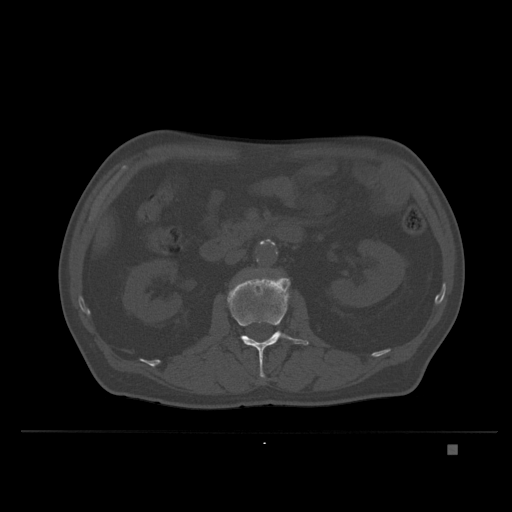
CT including the spine, one axial slice. Position 116 of 435 along the scan axis. Bone window (W 1800 / L 400 HU). 512 × 512 image matrix, field of view 434 × 434 mm. Male patient, age 73 years. From the clinical record (not read from this slice): primary cancer: skin.
Structures marked on this image (semi-automatic segmentation, software-assisted and operator-edited):
- L2 vertebra: bounding box (x1, y1, x2, y2) in pixels: (214, 276, 309, 382)